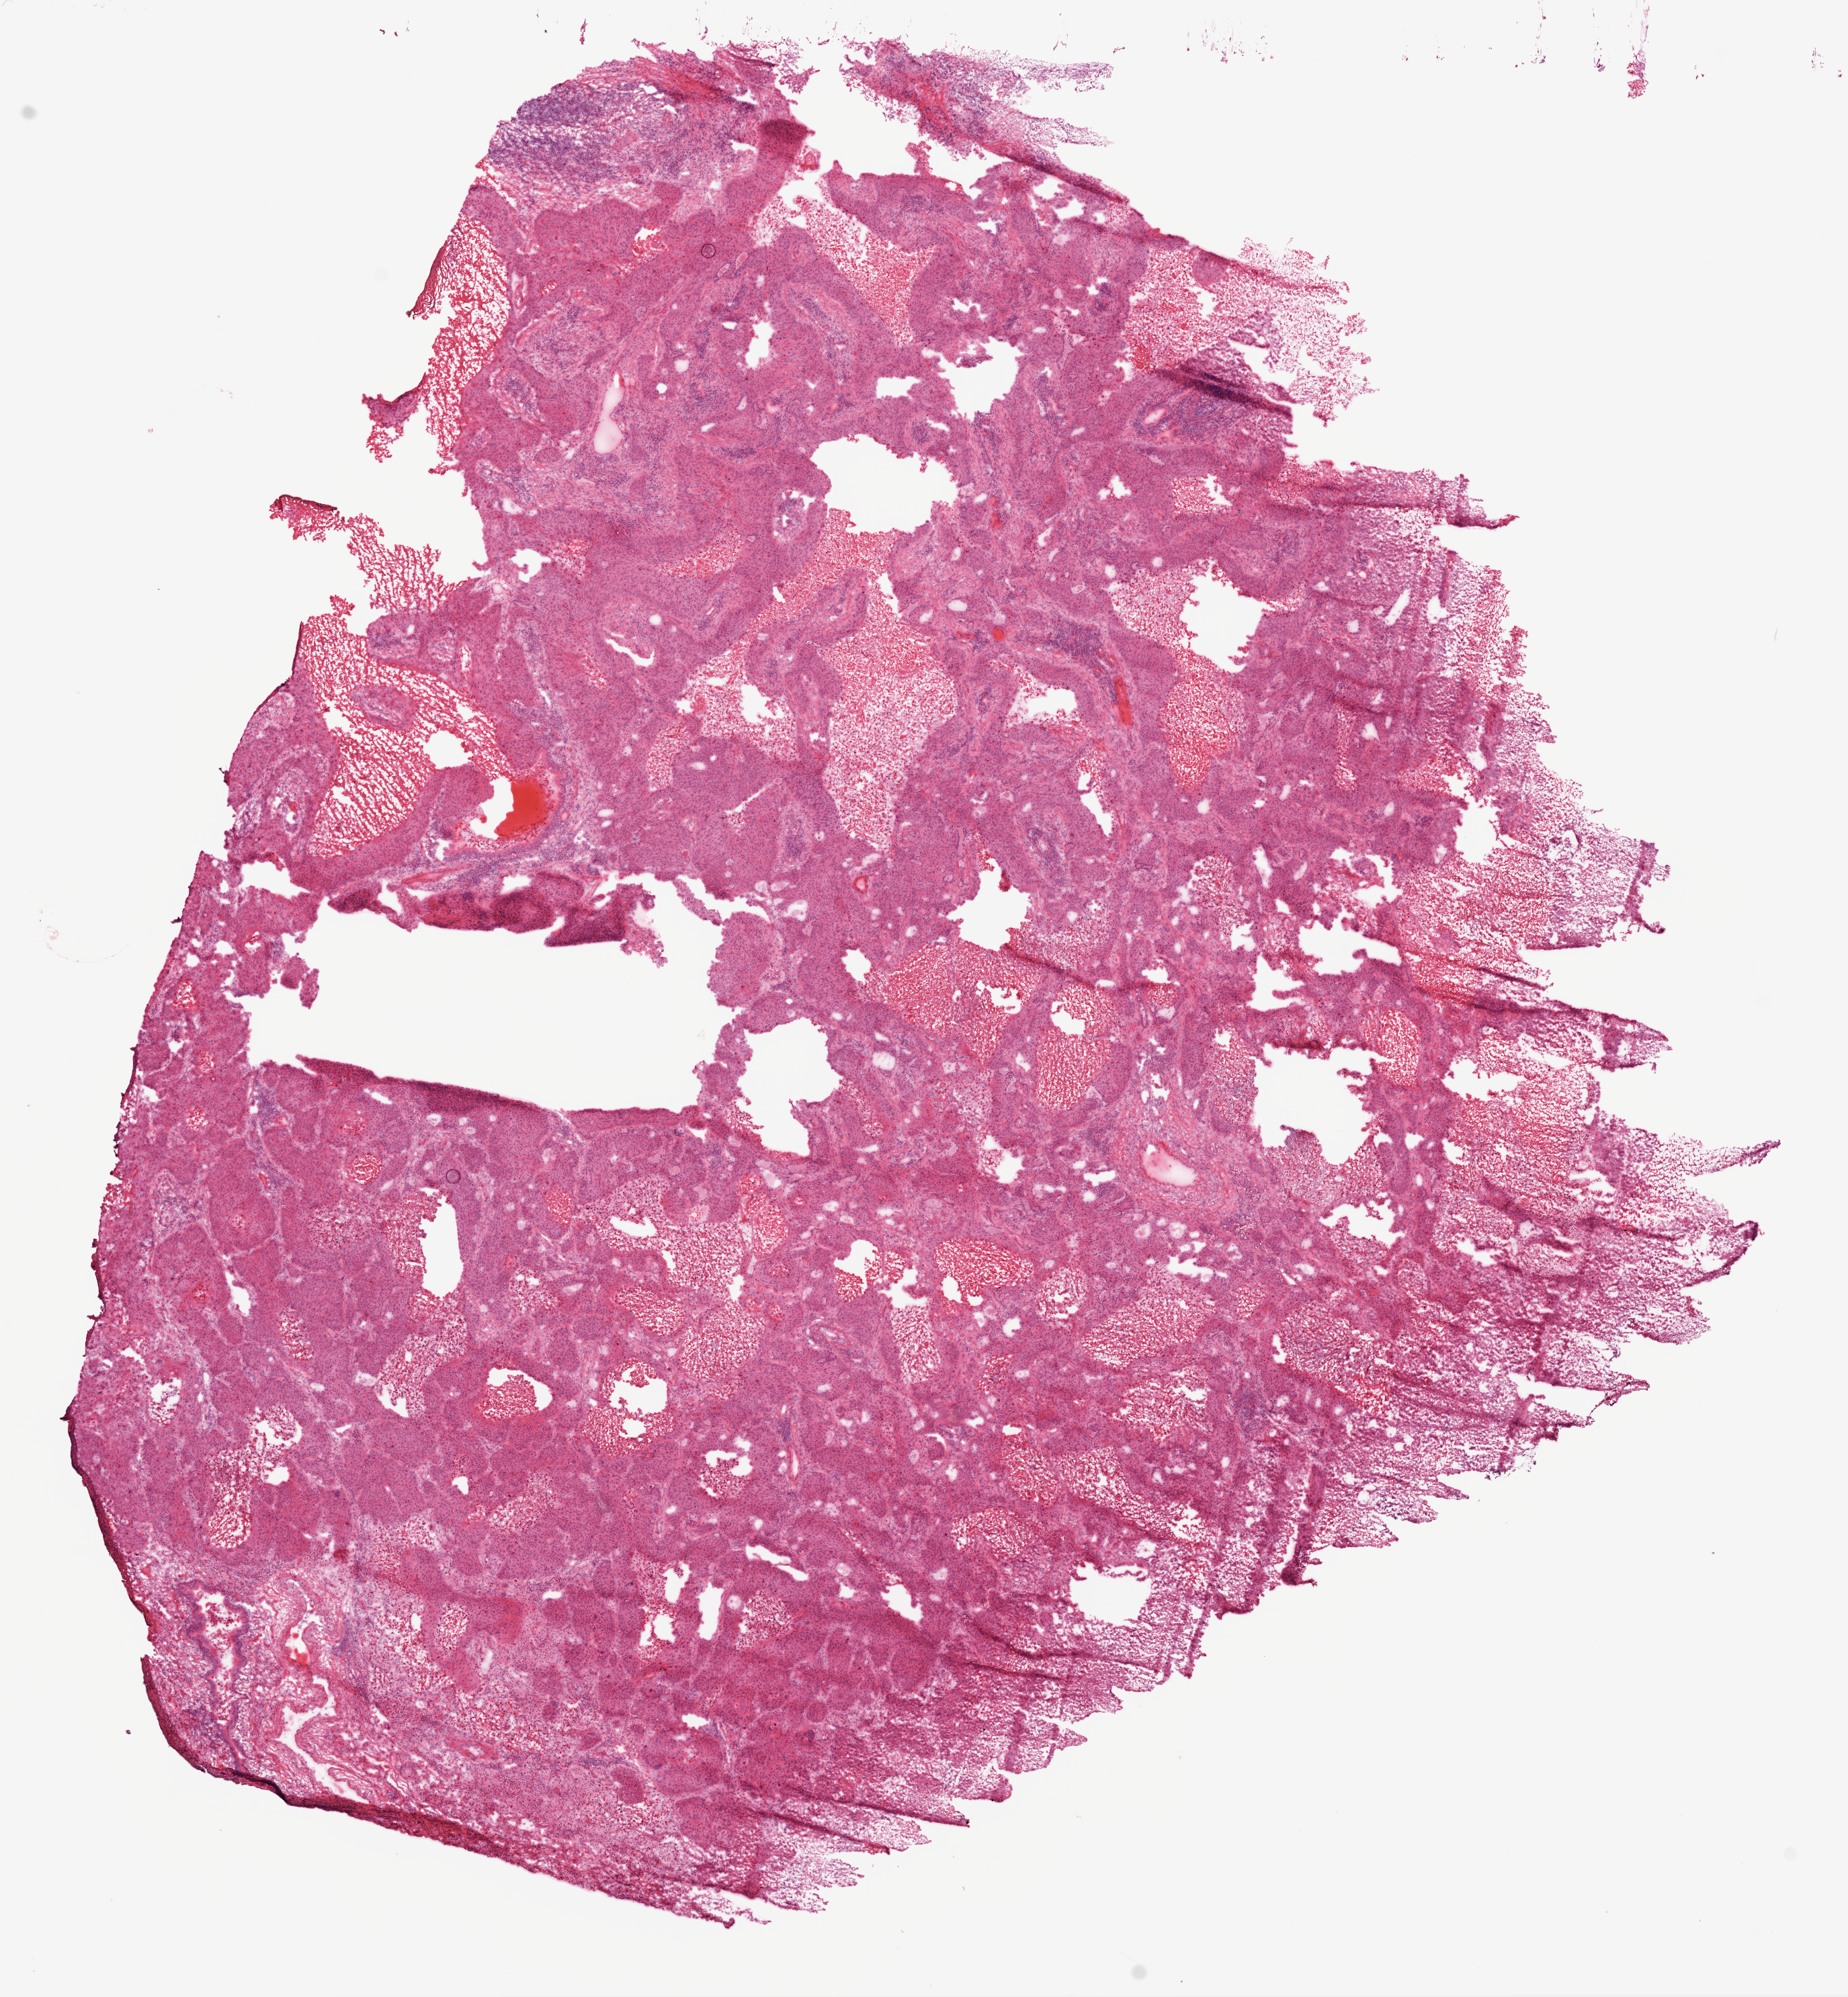
Digitized H&E-stained tissue section (whole slide), whole scanned area (about 11.0 x 11.9 mm, acquisition: 20x scan) shown as a low-resolution overview, frozen section from the top of the tissue portion, primary tumour sample from the lung. Patient: male, age at initial diagnosis 78 years. Composition of this section per pathologist review: tumour cells 60%, tumour nuclei 80%, normal cells 2%, stromal cells 18%, necrosis 20%. Inflammatory infiltration, as recorded: lymphocyte infiltration 5%, monocyte infiltration 0%, neutrophil infiltration 0%.
• diagnosis: Squamous cell carcinoma, NOS